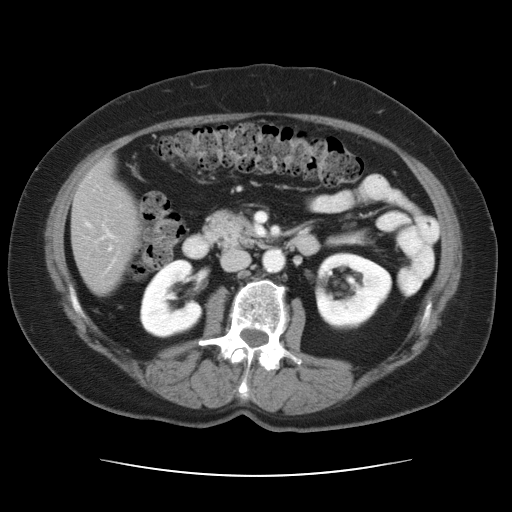
Contrast-enhanced abdominal CT, one axial slice. Position 11 of 34 along the scan axis. Reconstruction kernel STANDARD. 120 kVp. Intravenous contrast given. Soft-tissue window (W 400 / L 40 HU). 7.5 mm slice thickness. 512 × 512 image matrix, field of view 360 × 360 mm. Female patient, age 65 years. Case-level facts recorded for this patient, not image findings: diagnosis: colorectal cancer liver metastases, imaged before liver resection; multiple liver metastases: yes; largest metastasis: 2.2 cm; disease in both lobes: no.
Structures marked on this image (expert manual segmentation):
- liver: box from (x=73, y=163) to (x=137, y=293) px
- planned liver remnant (the part of the liver to remain after resection): (x=73, y=163)–(x=137, y=293)